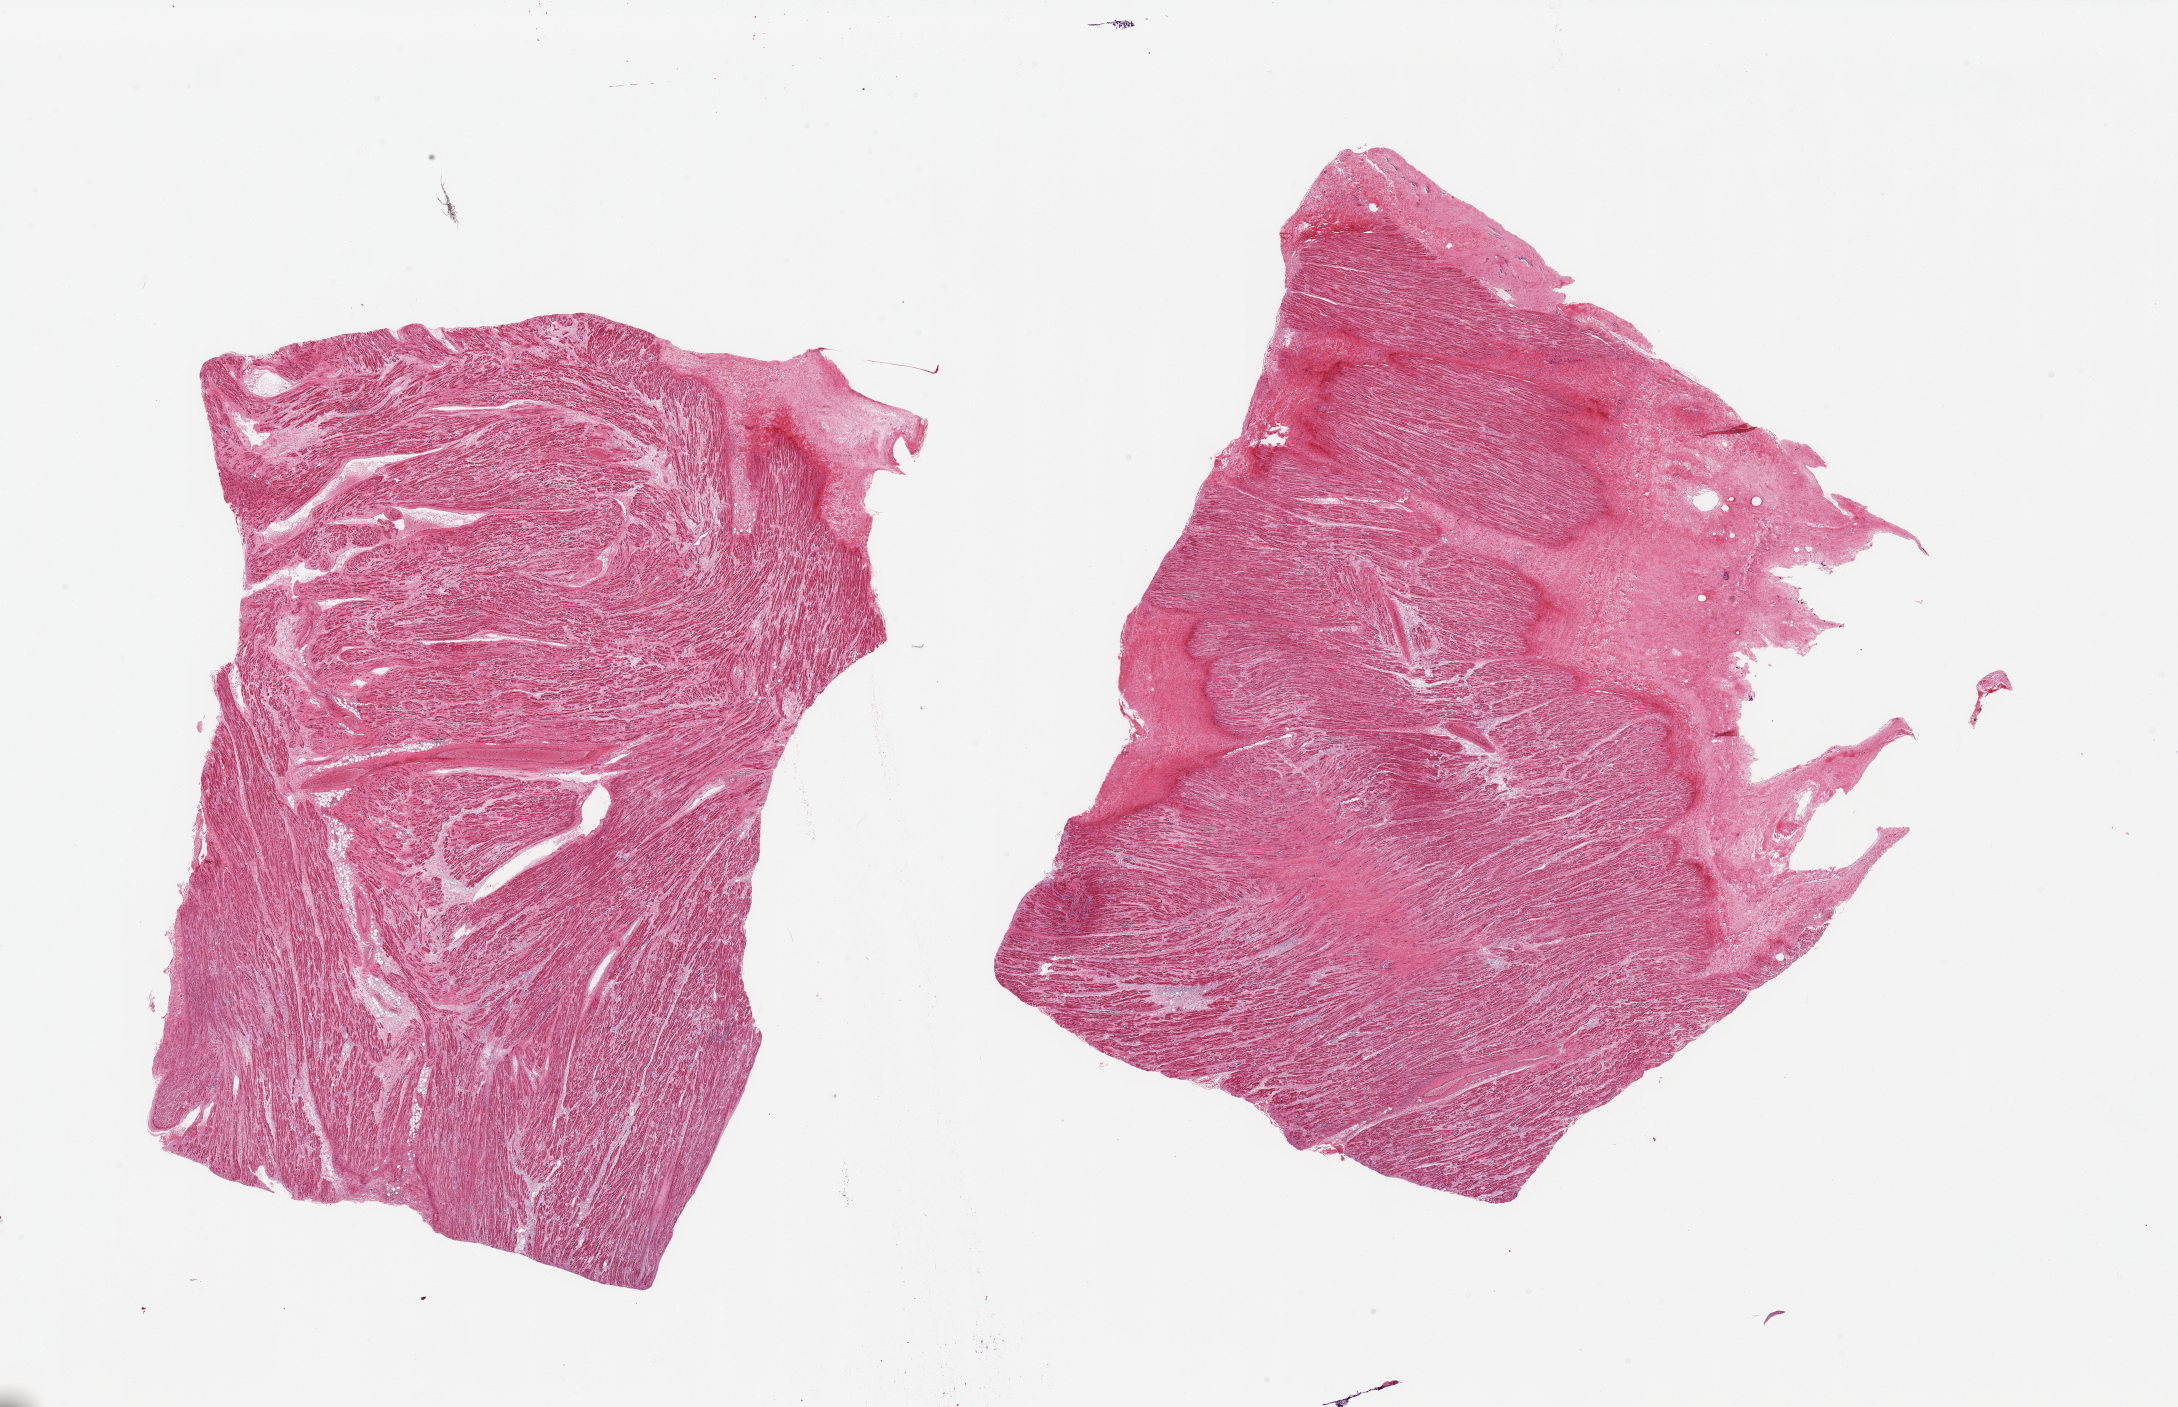
H&E whole-slide image, shown as a low-resolution overview of the whole scanned area (about 34.5 x 22.3 mm), PAXgene-fixed paraffin-embedded (PFPE) section, target tissue: auricular appendage, tissue donor sample. Donor: male.
Pathologist's review note for this sample: 2 pieces; 30% & 10% fibrous content.